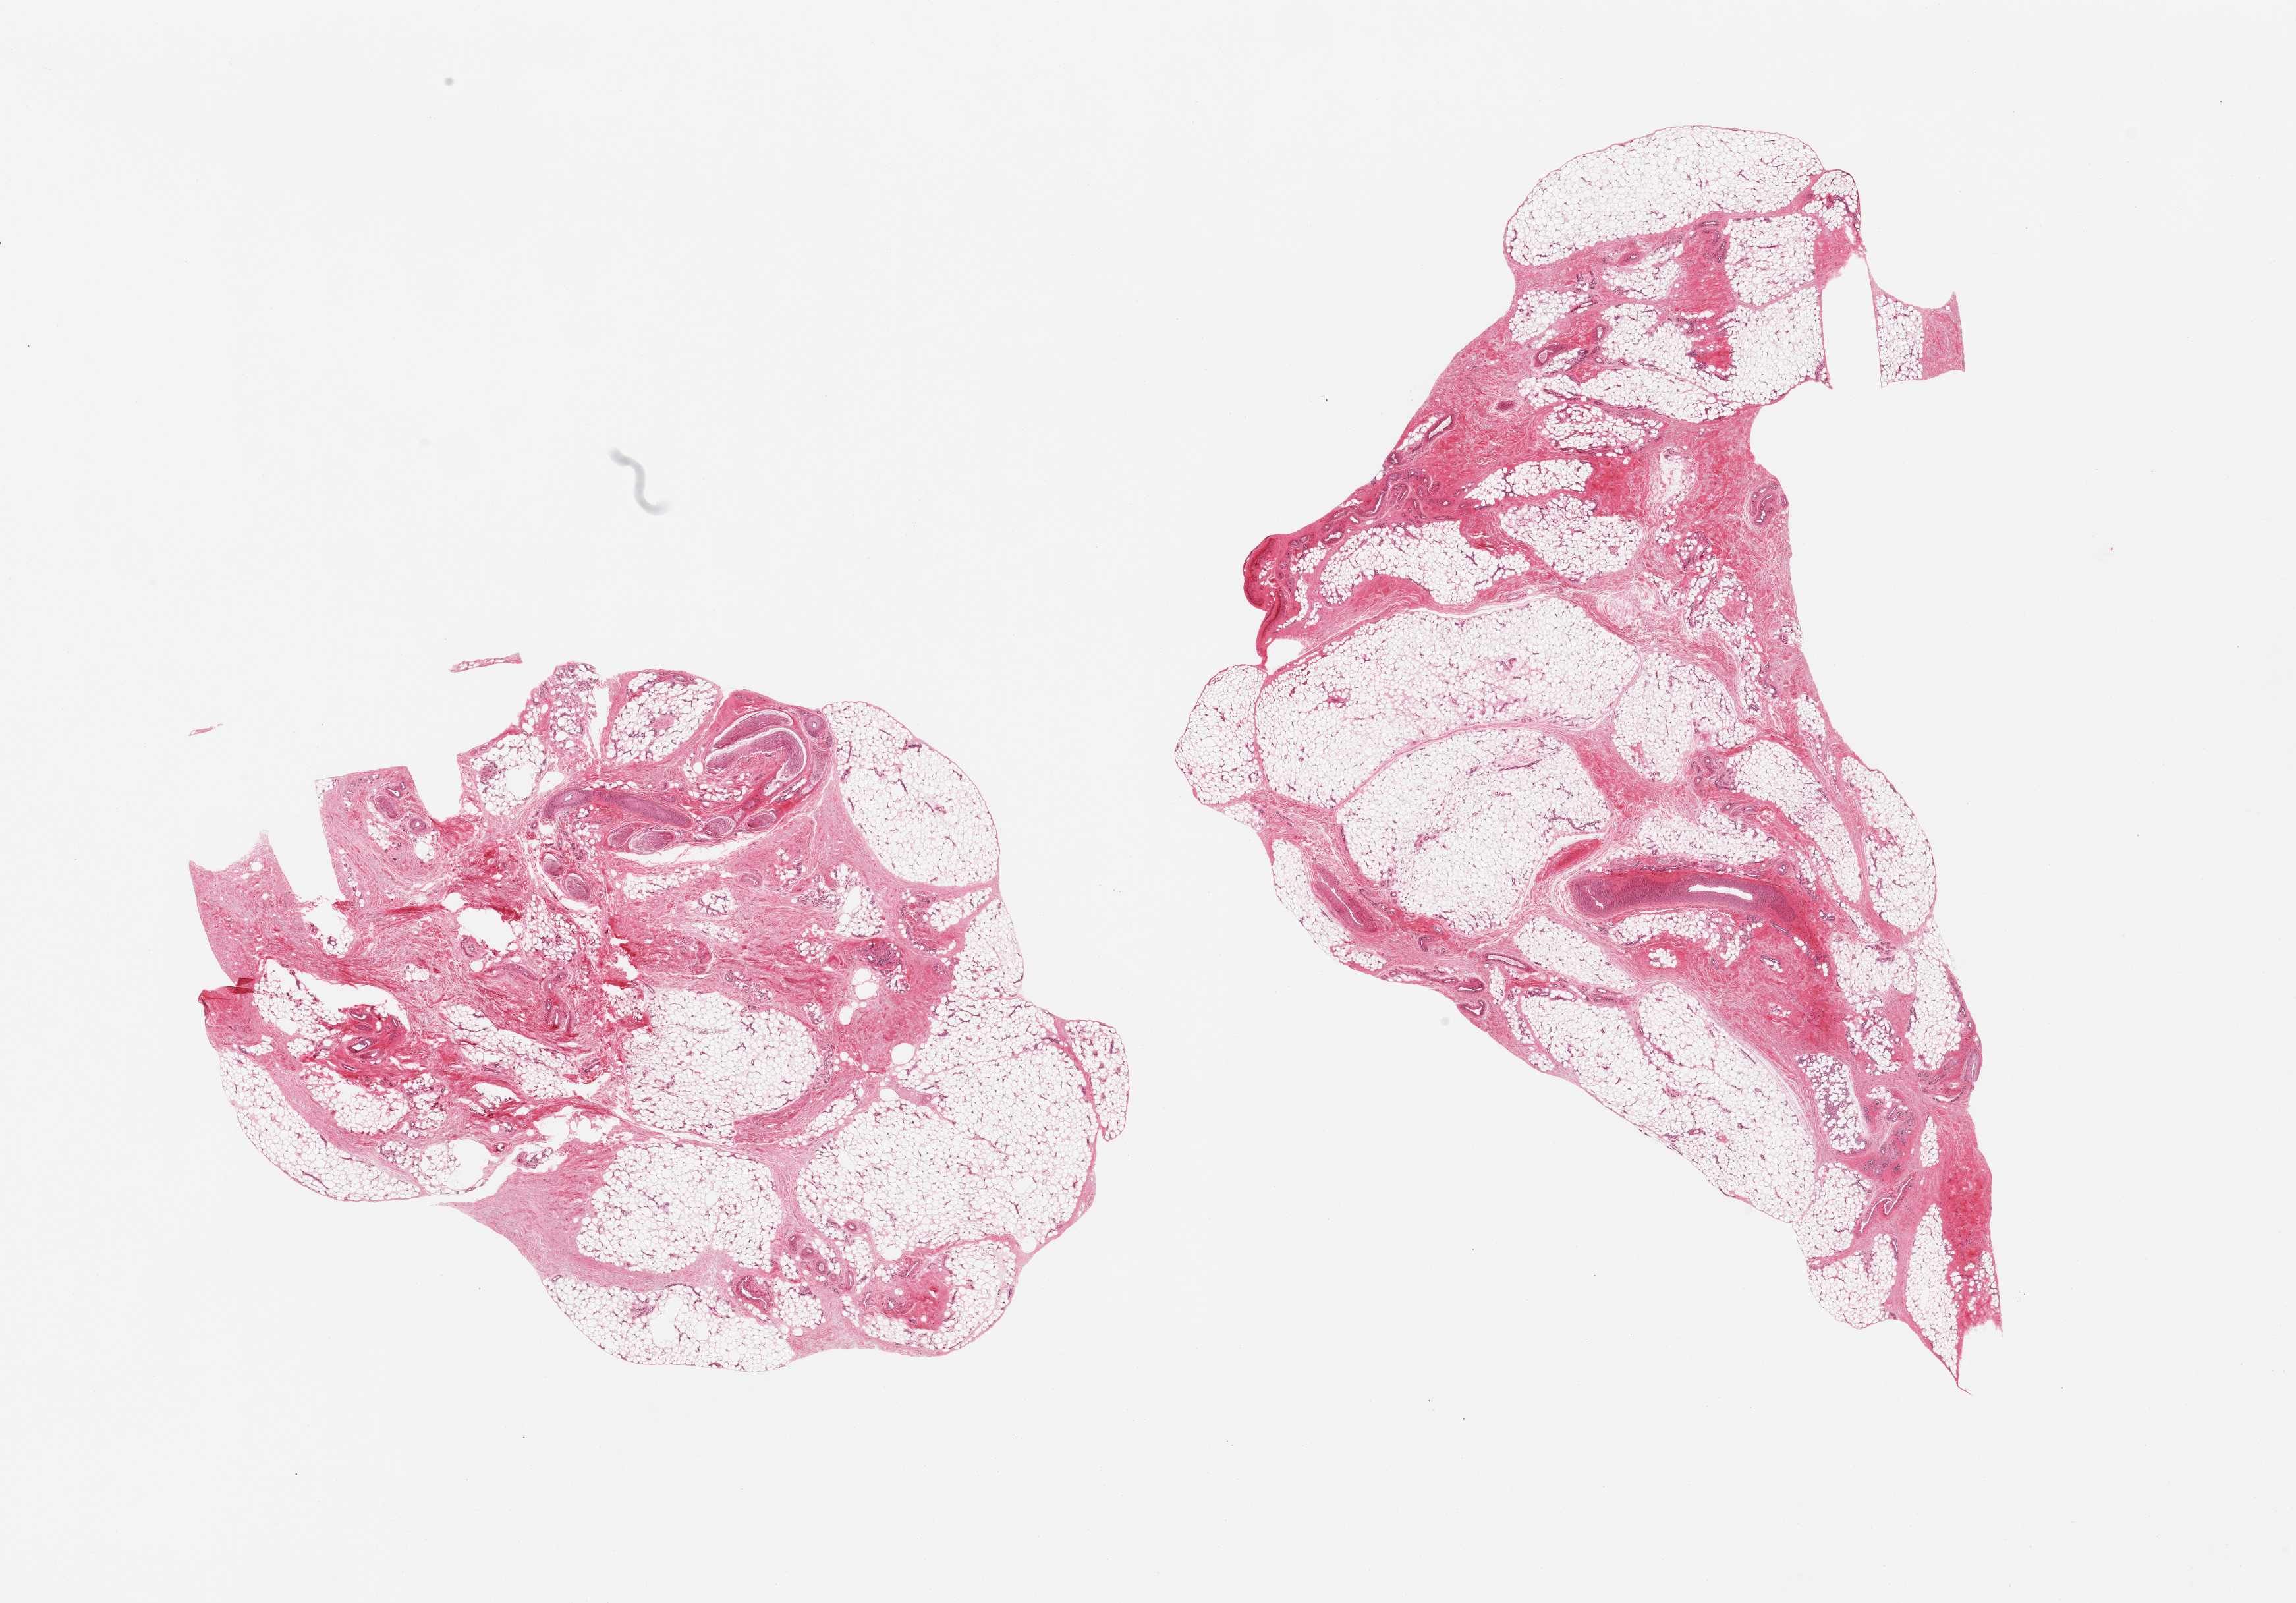
Whole-slide image, haematoxylin and eosin stain — shown as a low-resolution overview of the whole scanned area (about 27.6 x 19.2 mm, acquisition: 20x scan); PAXgene-fixed, paraffin-embedded tissue; section of adipose tissue (target tissue); donor tissue sample. Donor sex: male.
* review note (as recorded): 2 pieces; fat admixed with 30% and 50% fibrovascular tissue and in one piece, nerve